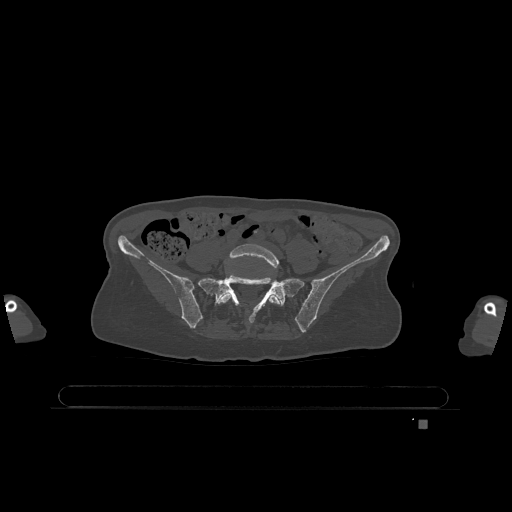
CT including the spine, one axial slice; position 211 of 1317 along the scan axis; bone window (W 1800 / L 400 HU); 0.5 mm slice thickness; 512 × 512 image matrix, field of view 500 × 500 mm. Patient: female, 74 years. From the clinical record (not read from this slice): primary cancer: lung; vertebrae with lytic lesions (as recorded): T1, T4, T5, T6, L4, L5.
Annotated regions visible in this slice (semi-automatically segmented with operator editing):
- L5 vertebra: bounding box [x1, y1, x2, y2] px = [218, 244, 282, 312]